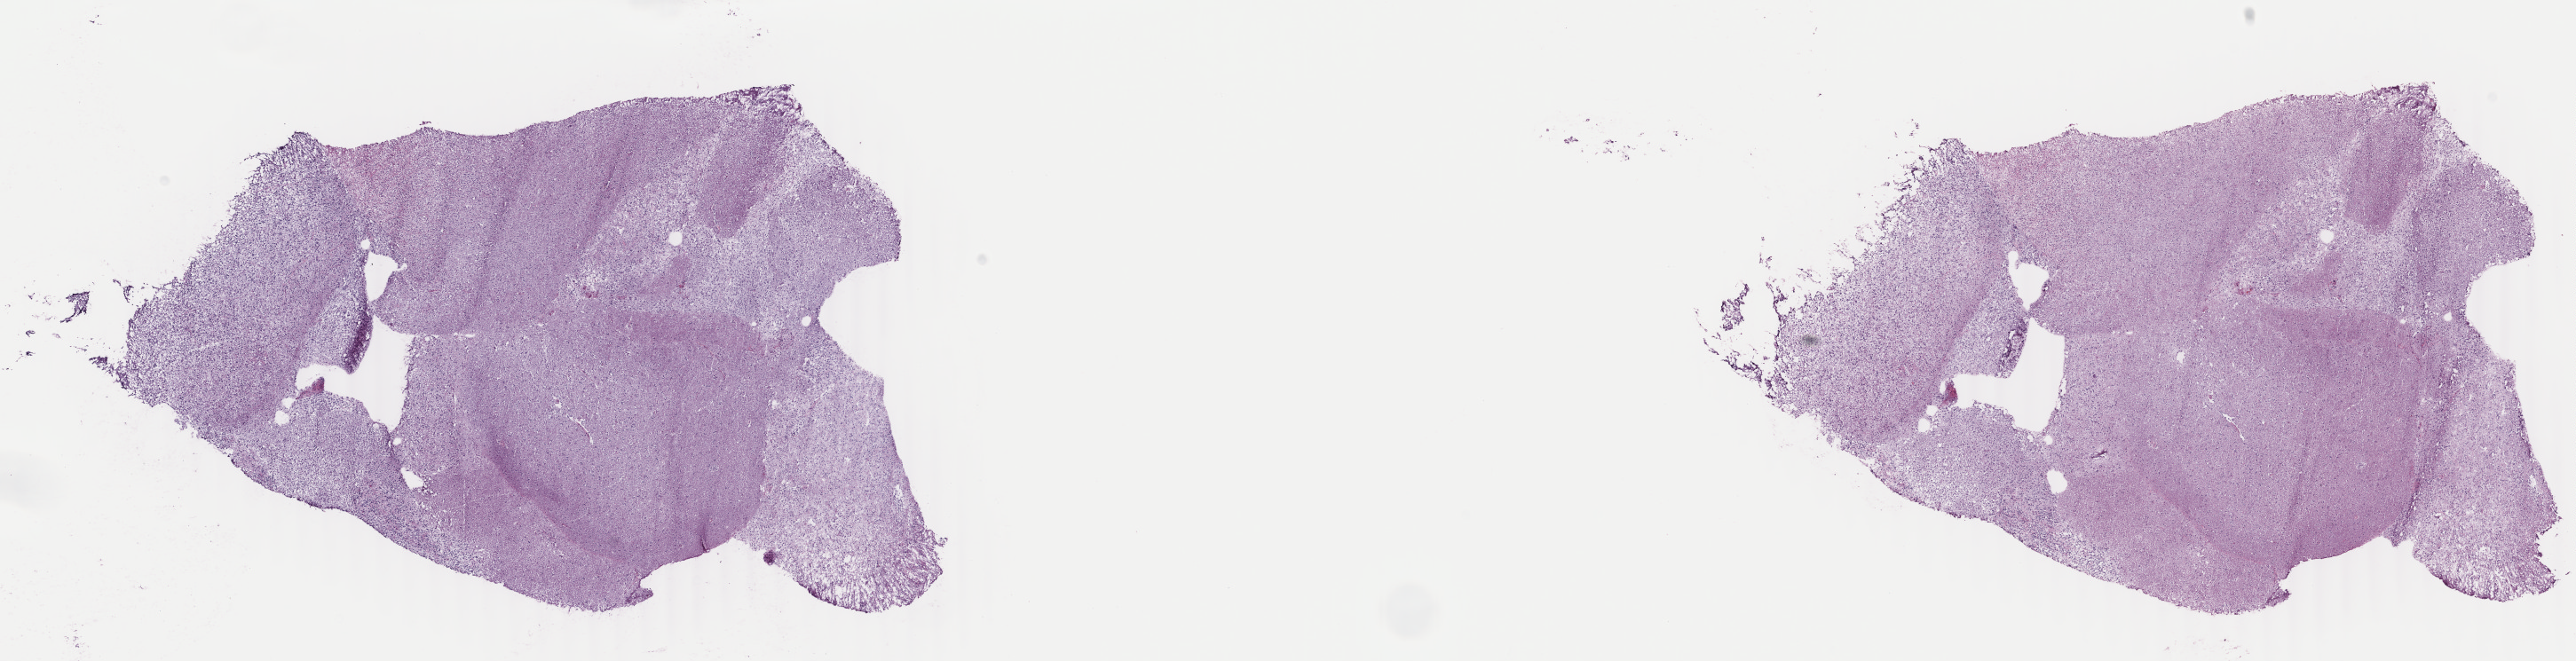
Whole-slide histology image, Hematoxylin and eosin (H&E) stained — a low-resolution overview of the entire scanned area, about 23.1 x 5.9 mm, frozen section from the top of the tissue portion, primary tumour sample from the brain. Male, age 41 years at initial diagnosis. Histologic grade: G2 (moderately differentiated). Composition of this section per pathologist review: tumour cells 50%, tumour nuclei 90%, normal cells 10%, stromal cells 40%, necrosis 0%. Infiltration values recorded for this section: lymphocyte infiltration 0%, monocyte infiltration 0%, neutrophil infiltration 0%.
Laterality: left. Histologic diagnosis: Oligodendroglioma, NOS.